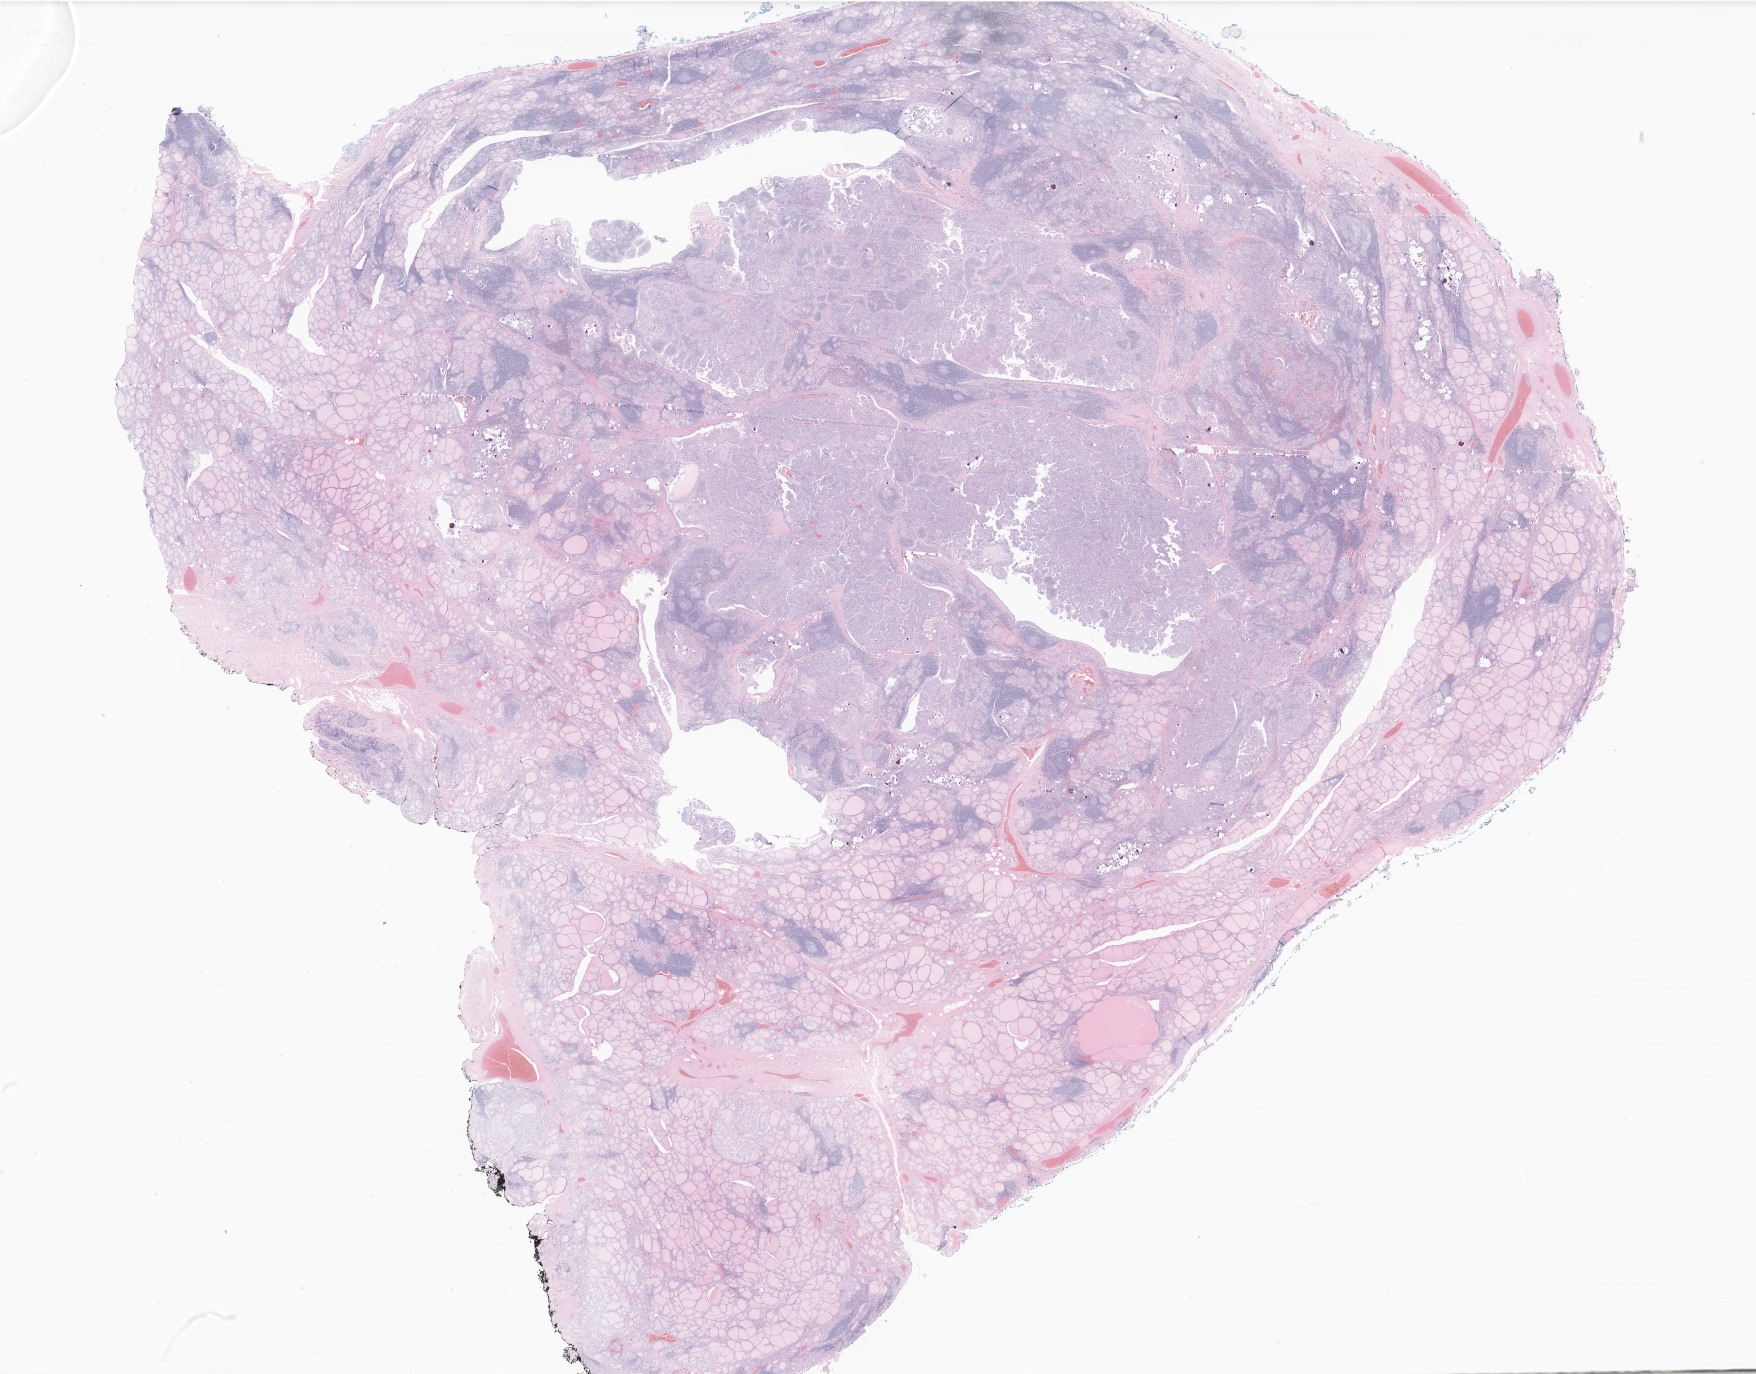
Haematoxylin and eosin whole-slide image of tumor tissue from the thyroid — shown as a low-resolution overview of the whole scanned area (about 29.6 x 23.2 mm), formalin-fixed paraffin-embedded section. Patient: female, age 150 months (12 years 6 months).
- recorded diagnosis: Carcinoma, NOS